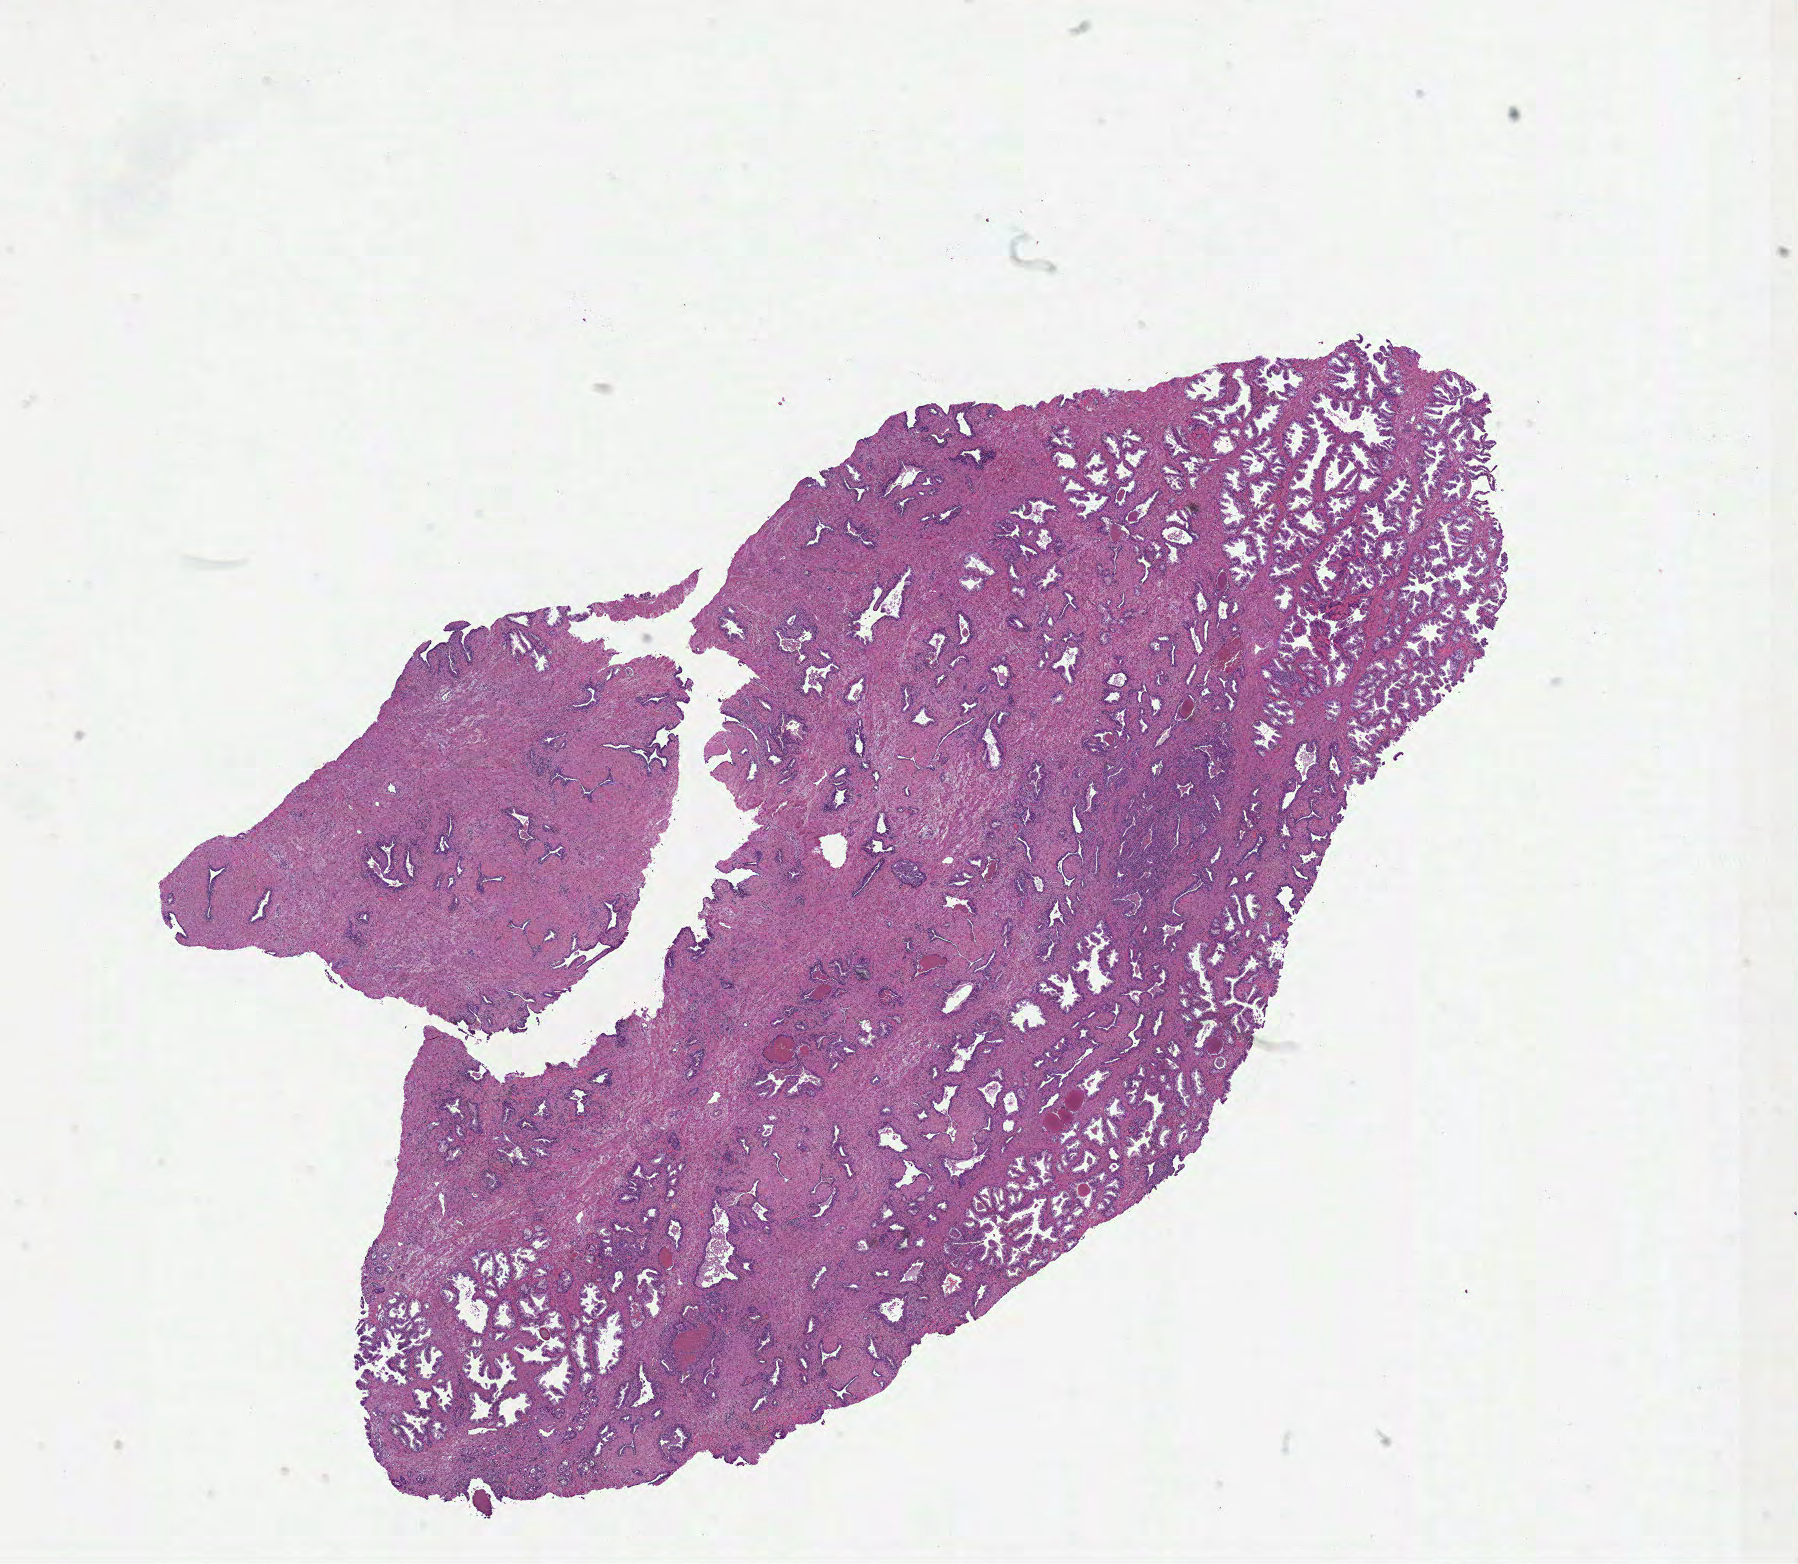
Digitized Hematoxylin and eosin (H&E) stained tissue section (whole slide), low-resolution overview of the scanned area, about 14.5 x 12.6 mm (acquisition: 40x scan), formalin-fixed paraffin-embedded (FFPE) diagnostic section, primary tumour sample from the prostate. Patient: male, age at initial diagnosis 52 years. Gleason score: 7 (3+4).
• laterality: bilateral
• diagnosis: Acinar cell carcinoma